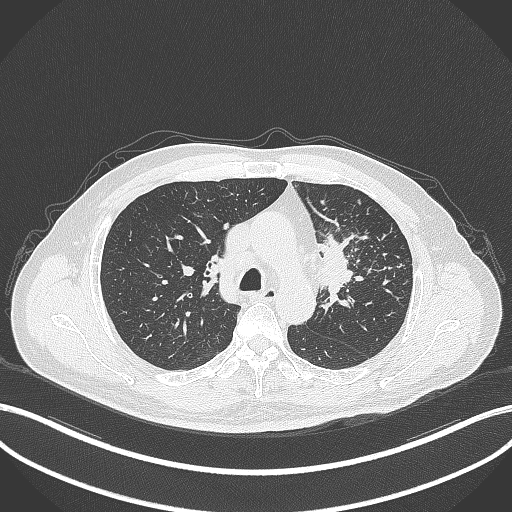
Chest CT, one axial slice; slice 241 of 386 in the series (ordered by position); reconstruction kernel B70f; 120 kVp; lung window (W 1500 / L -600 HU); 1 mm slice thickness; 512 × 512 image matrix, field of view 400 × 400 mm. Male patient, age 69 years. From the clinical record (not read from this slice): clinical TNM (as recorded): T2a N2 M0.
Structures marked on this image (rectangle marked by the reading radiologist):
- lung tumour (recorded histology: adenocarcinoma): box from (x=318, y=231) to (x=358, y=313) px